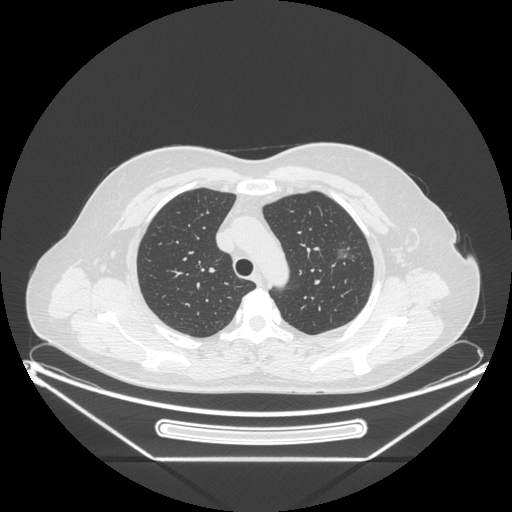
Chest CT, one axial slice; slice 167 of 226 in the series (ordered by position); reconstruction kernel STANDARD; lung window (W 1500 / L -600 HU); 1.25 mm slice thickness; 512 × 512 image matrix. Female patient, age 54 years. From the clinical record (not read from this slice): clinical TNM (as recorded): T1c N0 M0; histopathological grade: G1.
Outlined on this slice (rectangle marked by the reading radiologist):
- lung tumour (recorded histology: adenocarcinoma): bounding box <329,239,359,277> (left, top, right, bottom; pixels)